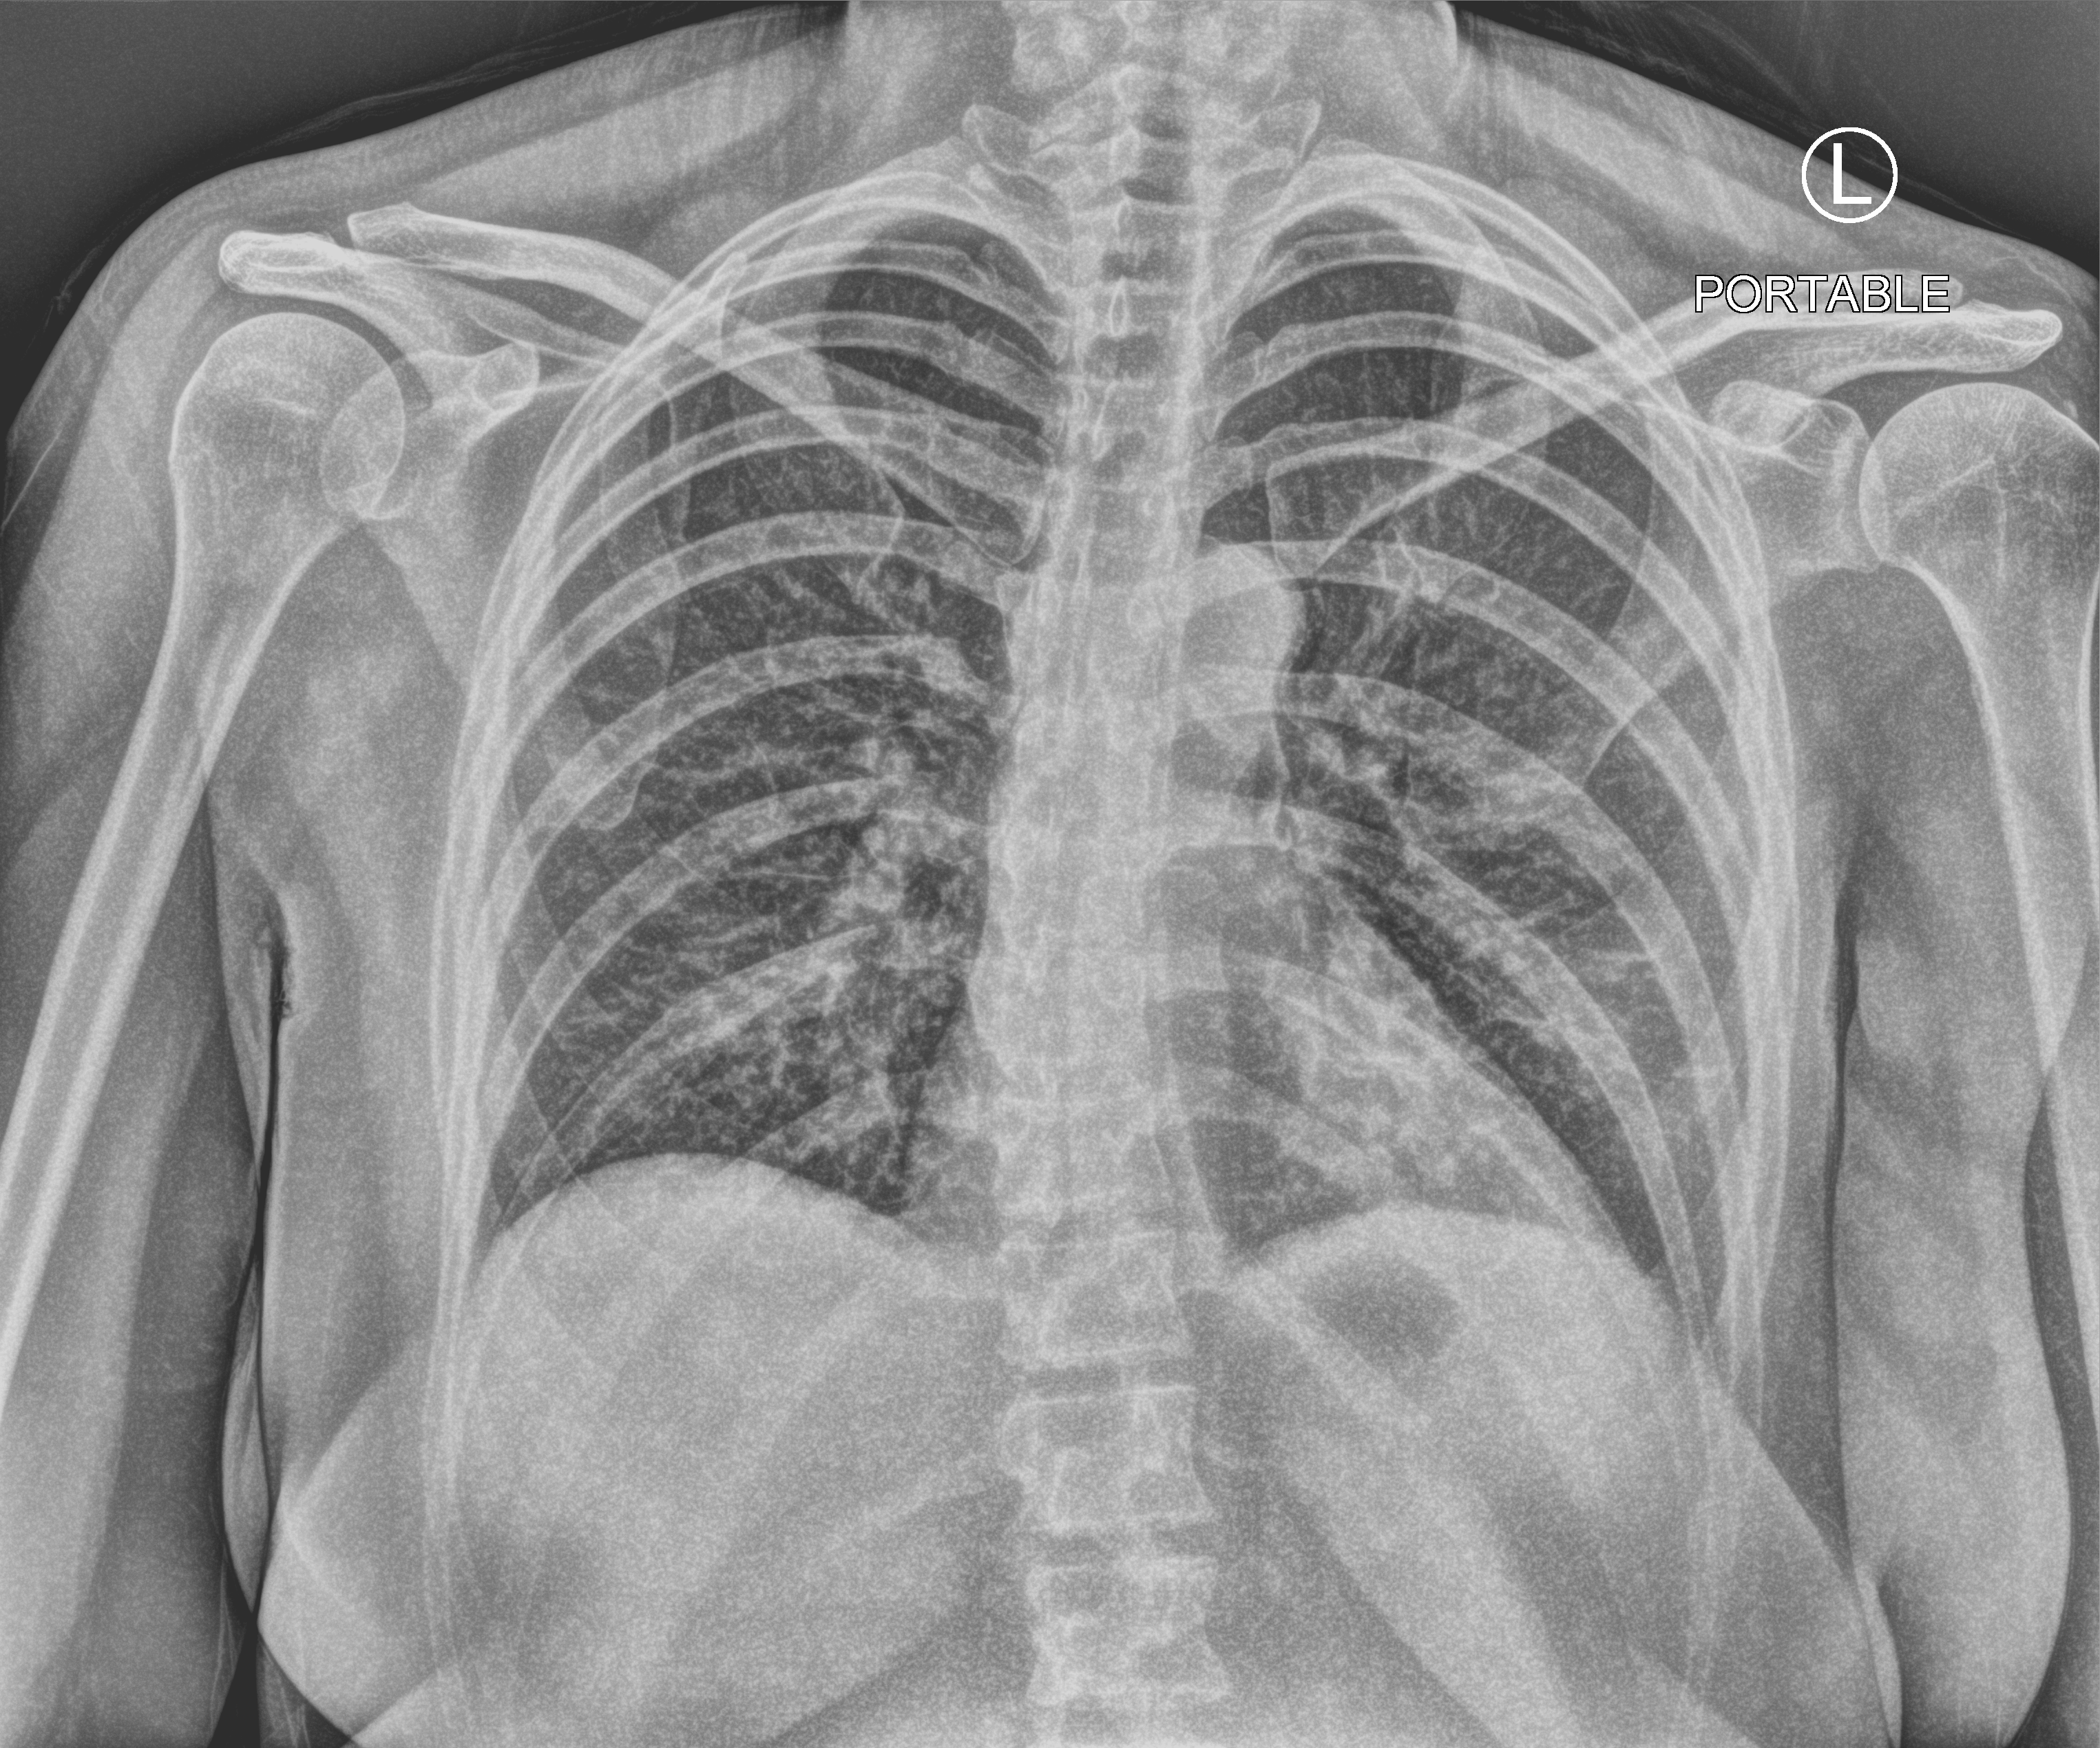
Bedside chest radiograph (computed radiography). Patient hospitalised with COVID-19; female, aged 18–59 years.
From the hospital-stay record, not from the radiograph (when in the stay this image was taken is not recorded):
- diabetes (admission record): no
- mechanically ventilated during this hospital stay: no